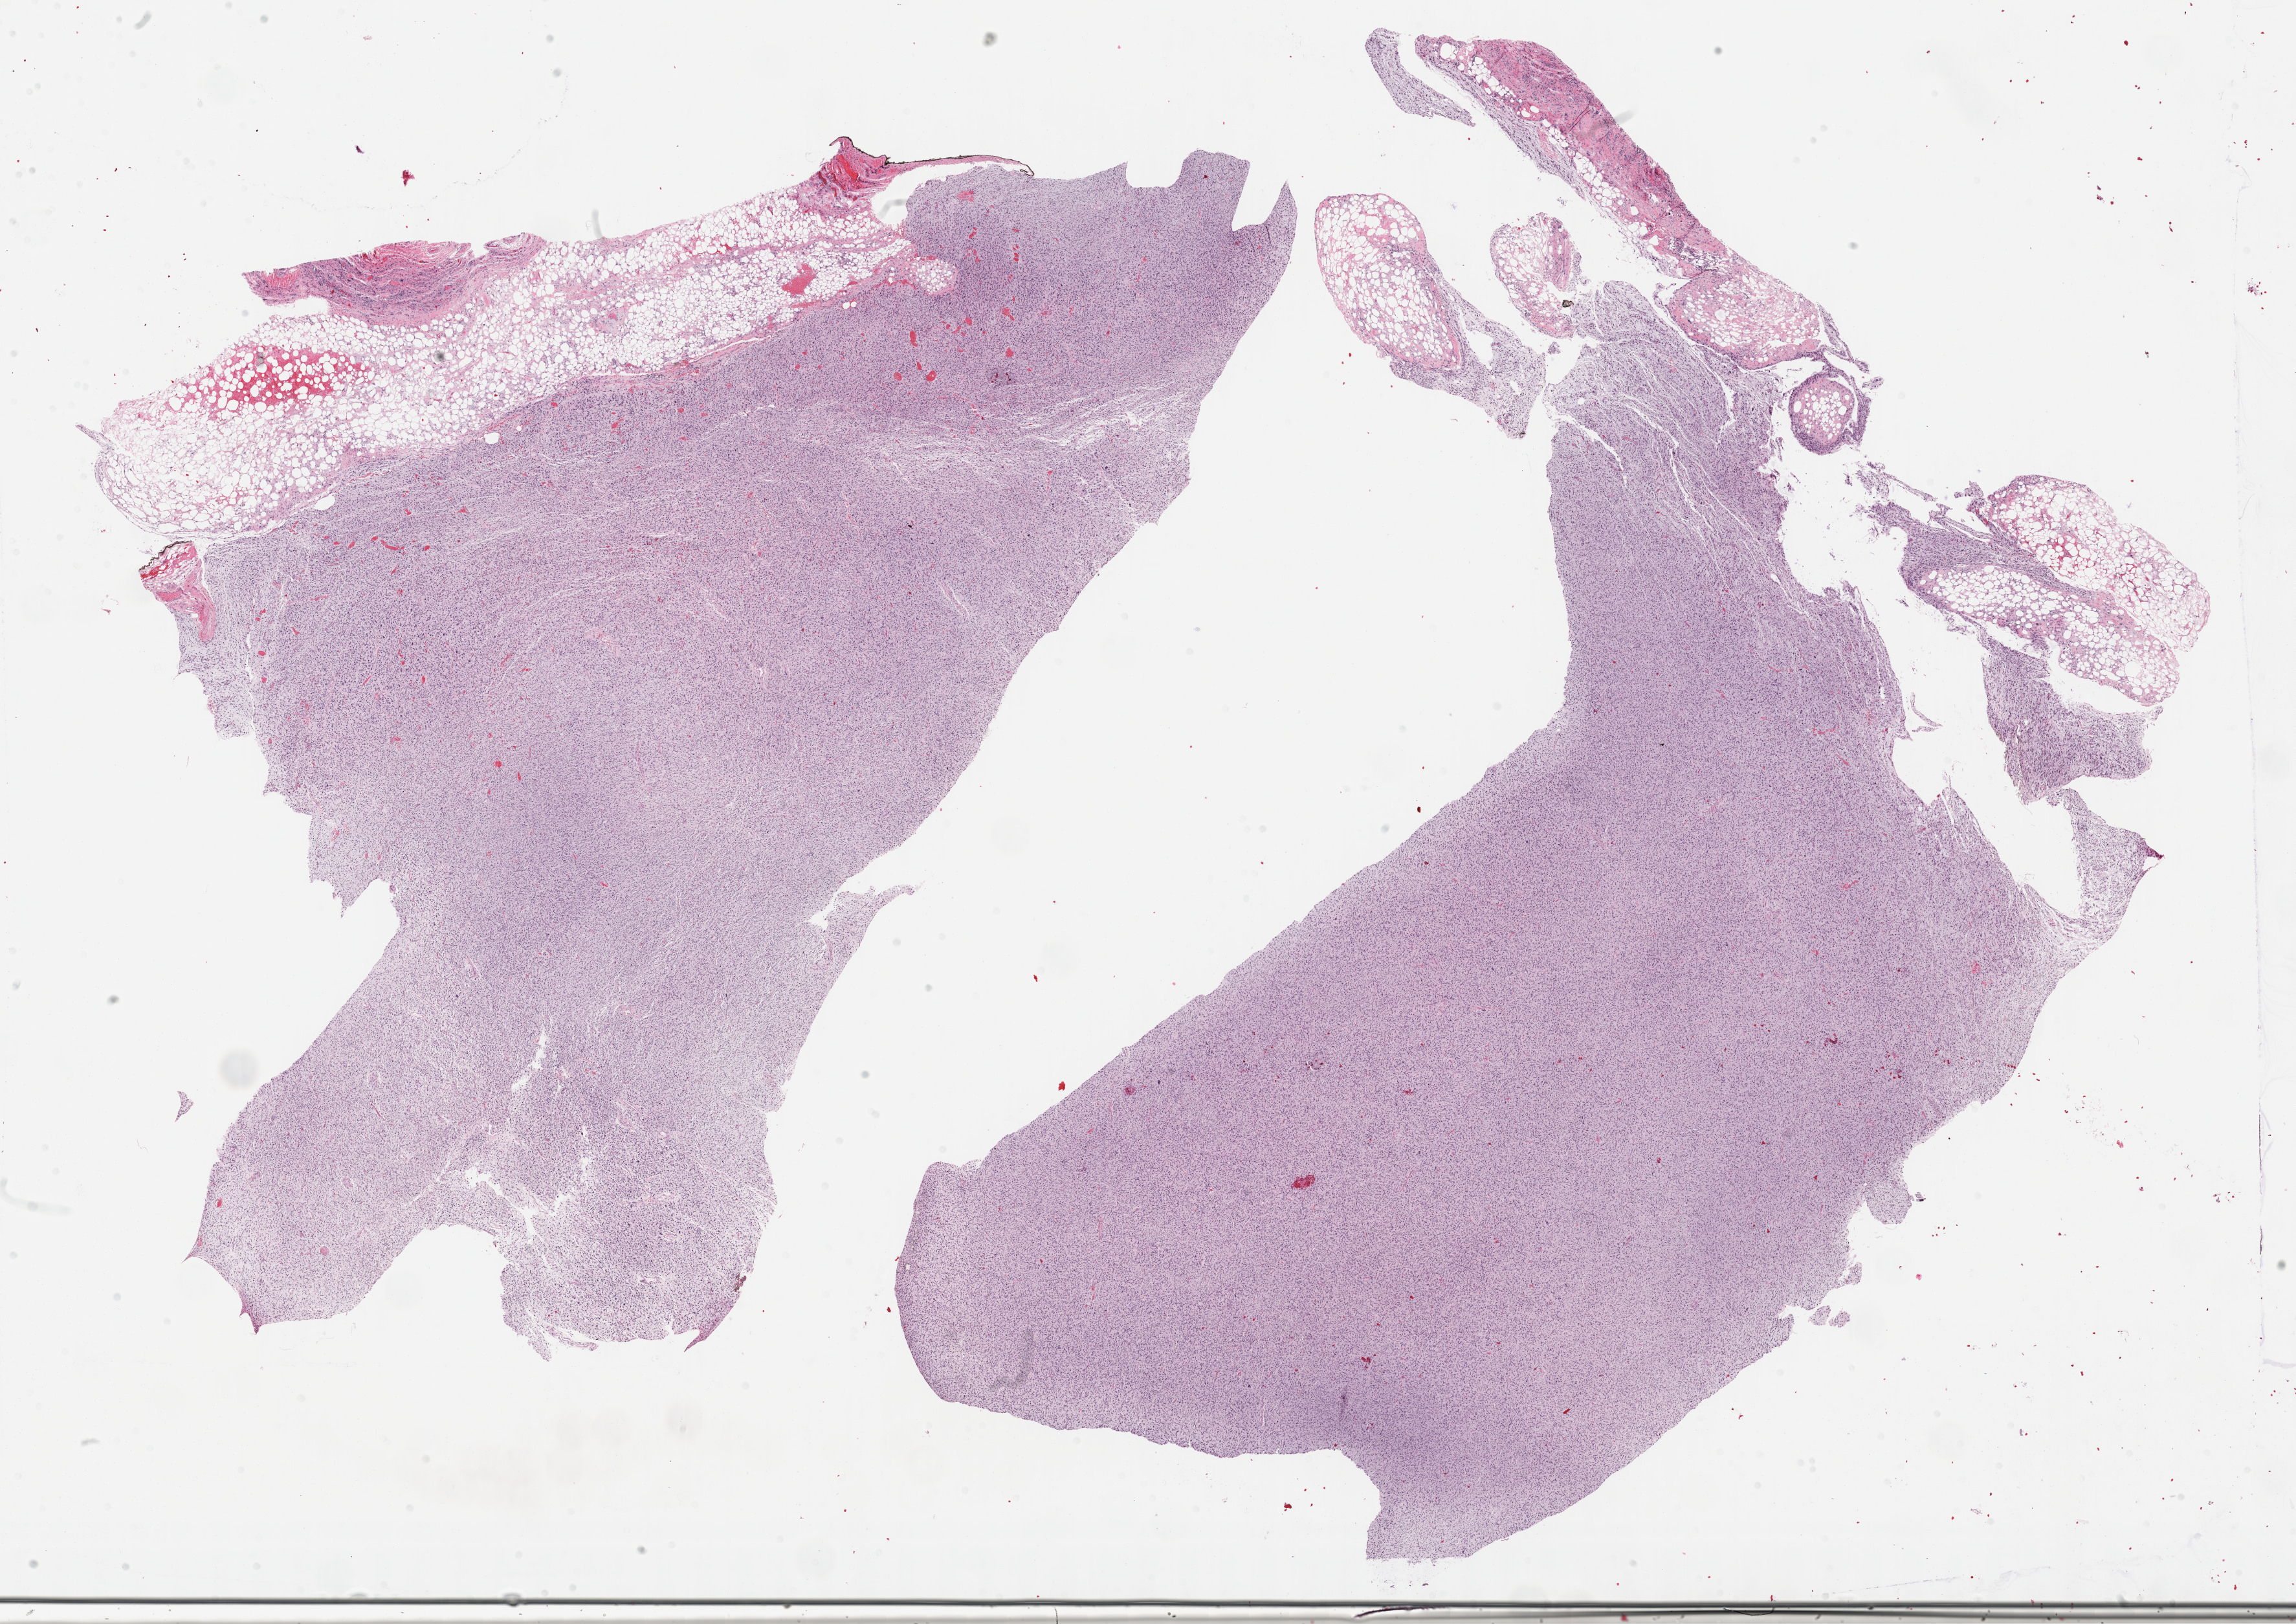
Digitized H&E-stained tissue section (whole slide), a low-resolution overview of the entire scanned area, about 28.7 x 20.3 mm (acquisition: 40x scan). FFPE section. Primary tumour sample from the colon. Male, age 65 years at initial diagnosis.
Histologic diagnosis: Dedifferentiated liposarcoma (descending colon).